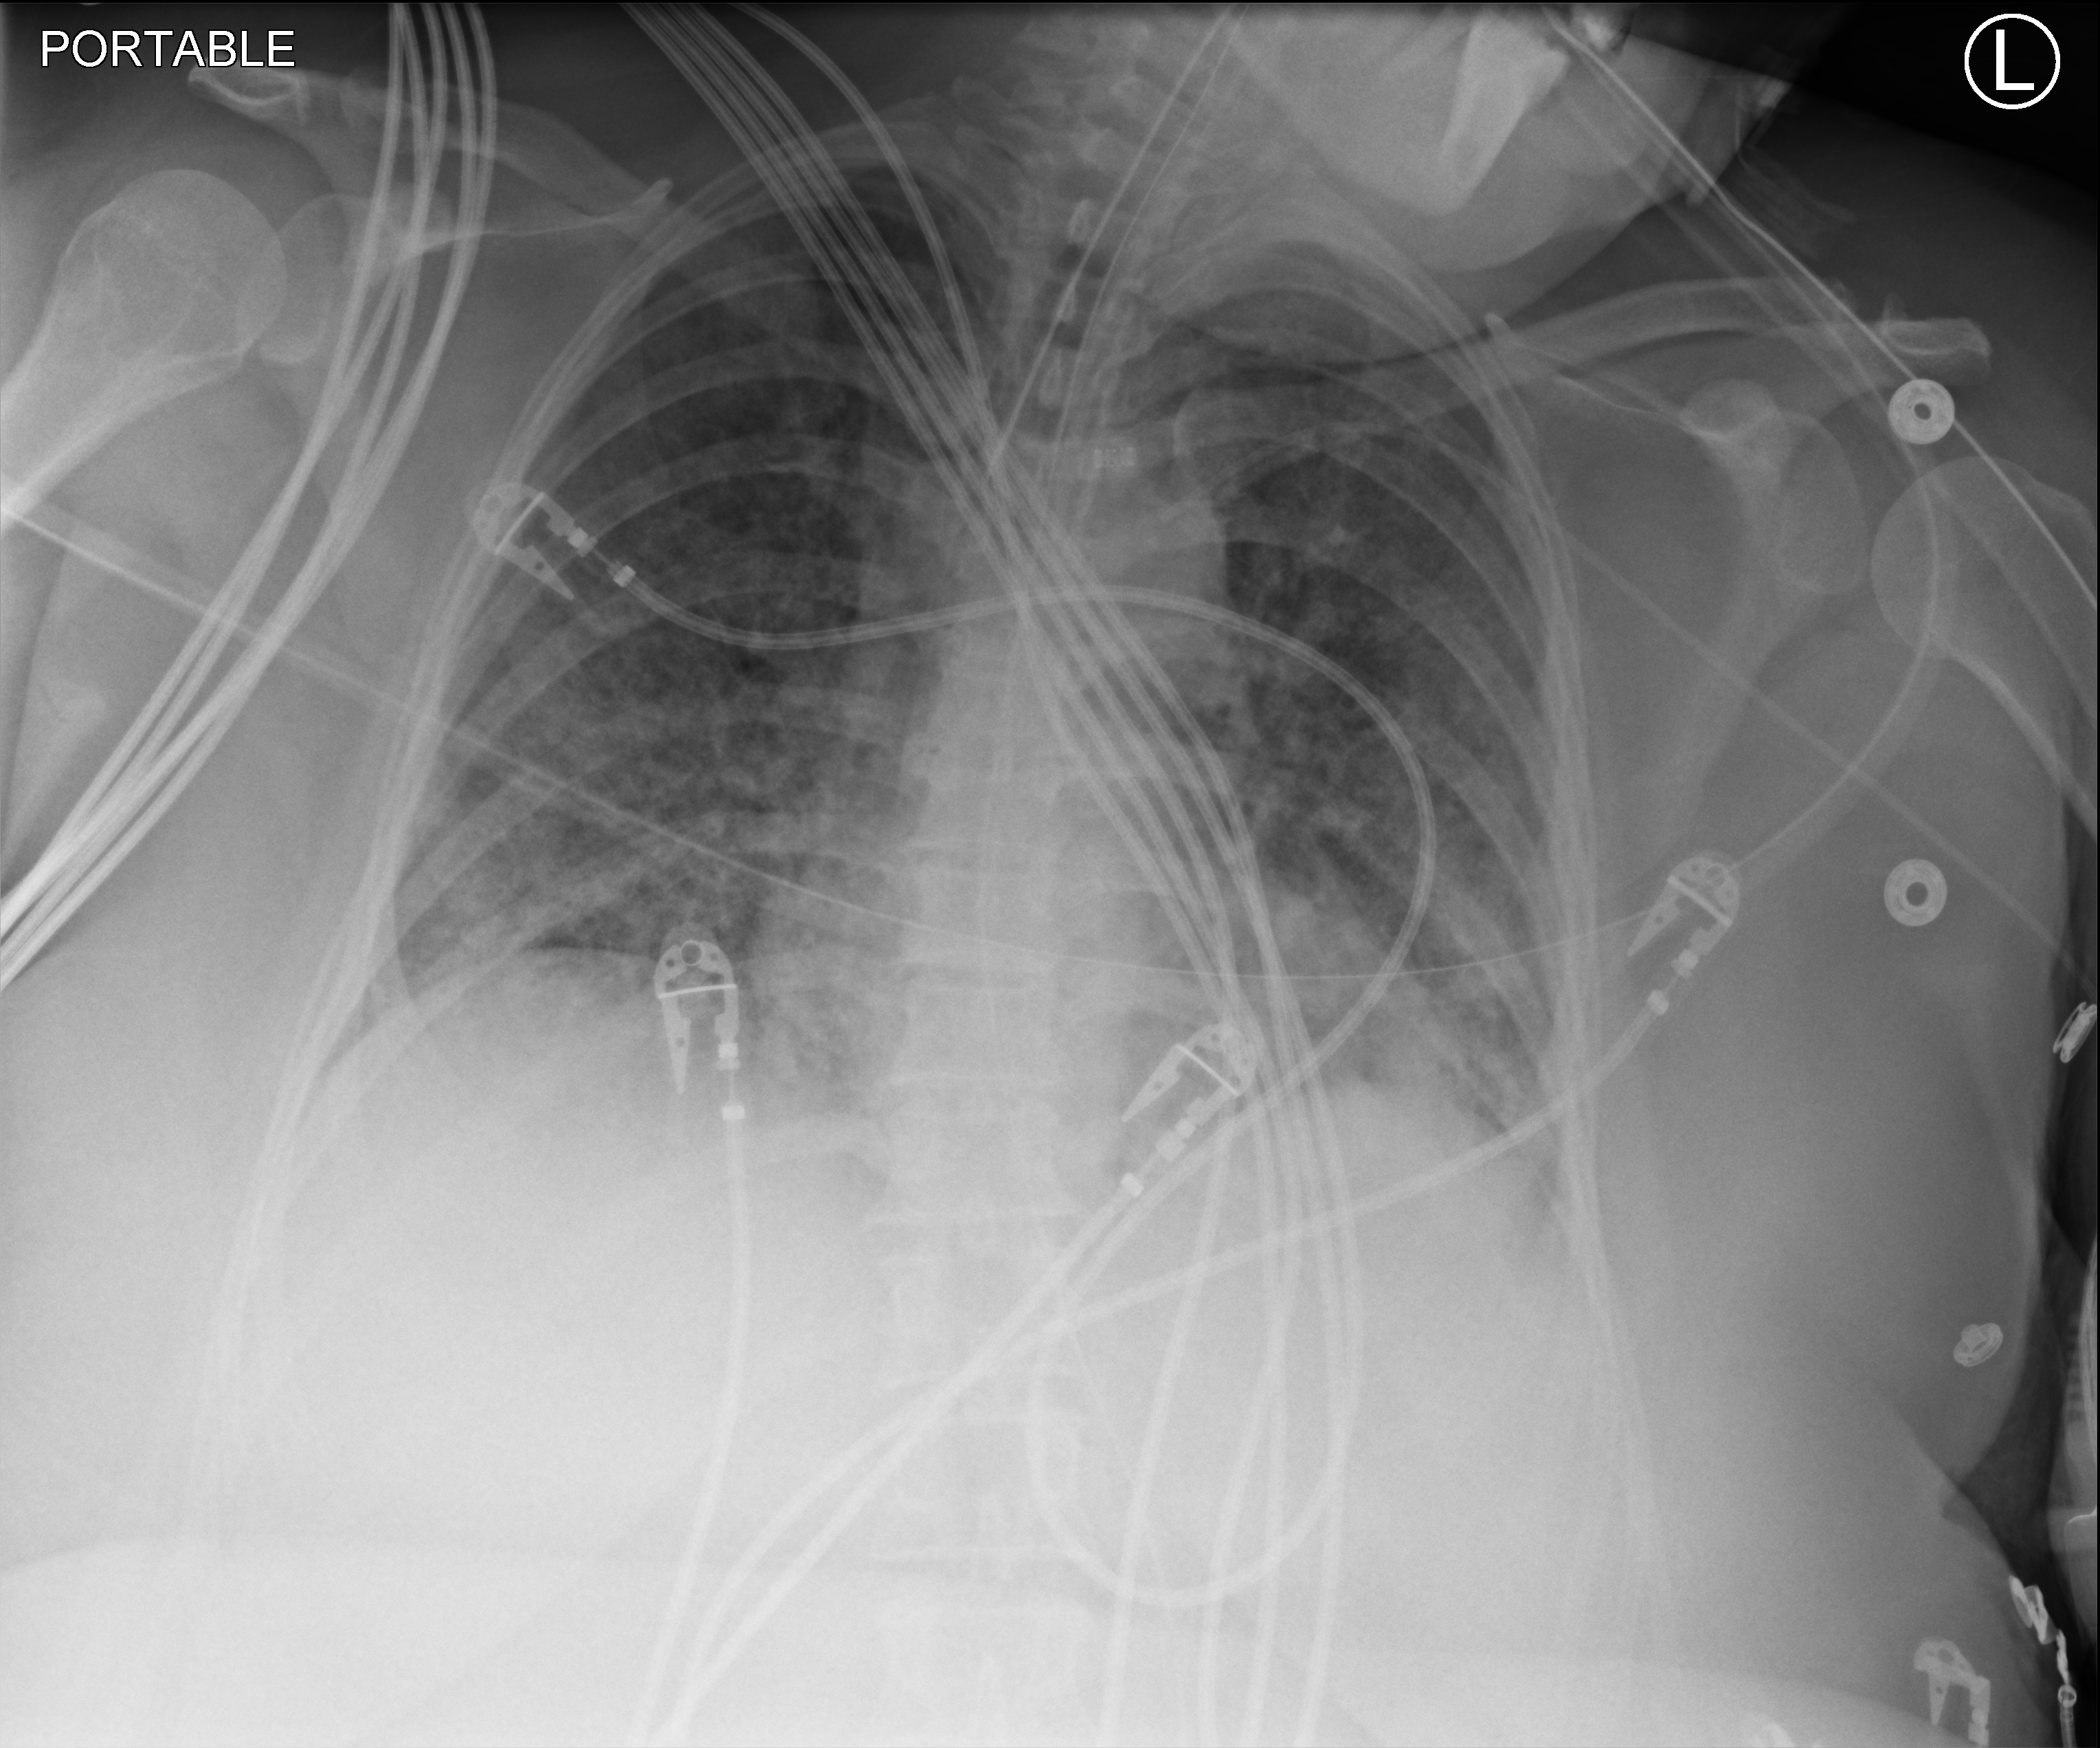
Bedside chest radiograph (computed radiography), anteroposterior (AP) projection. Patient hospitalised with COVID-19; female, aged 18–59 years.
Admission-level facts for this patient (not findings on this image; timing relative to this image not recorded): mechanically ventilated during this hospital stay: yes.